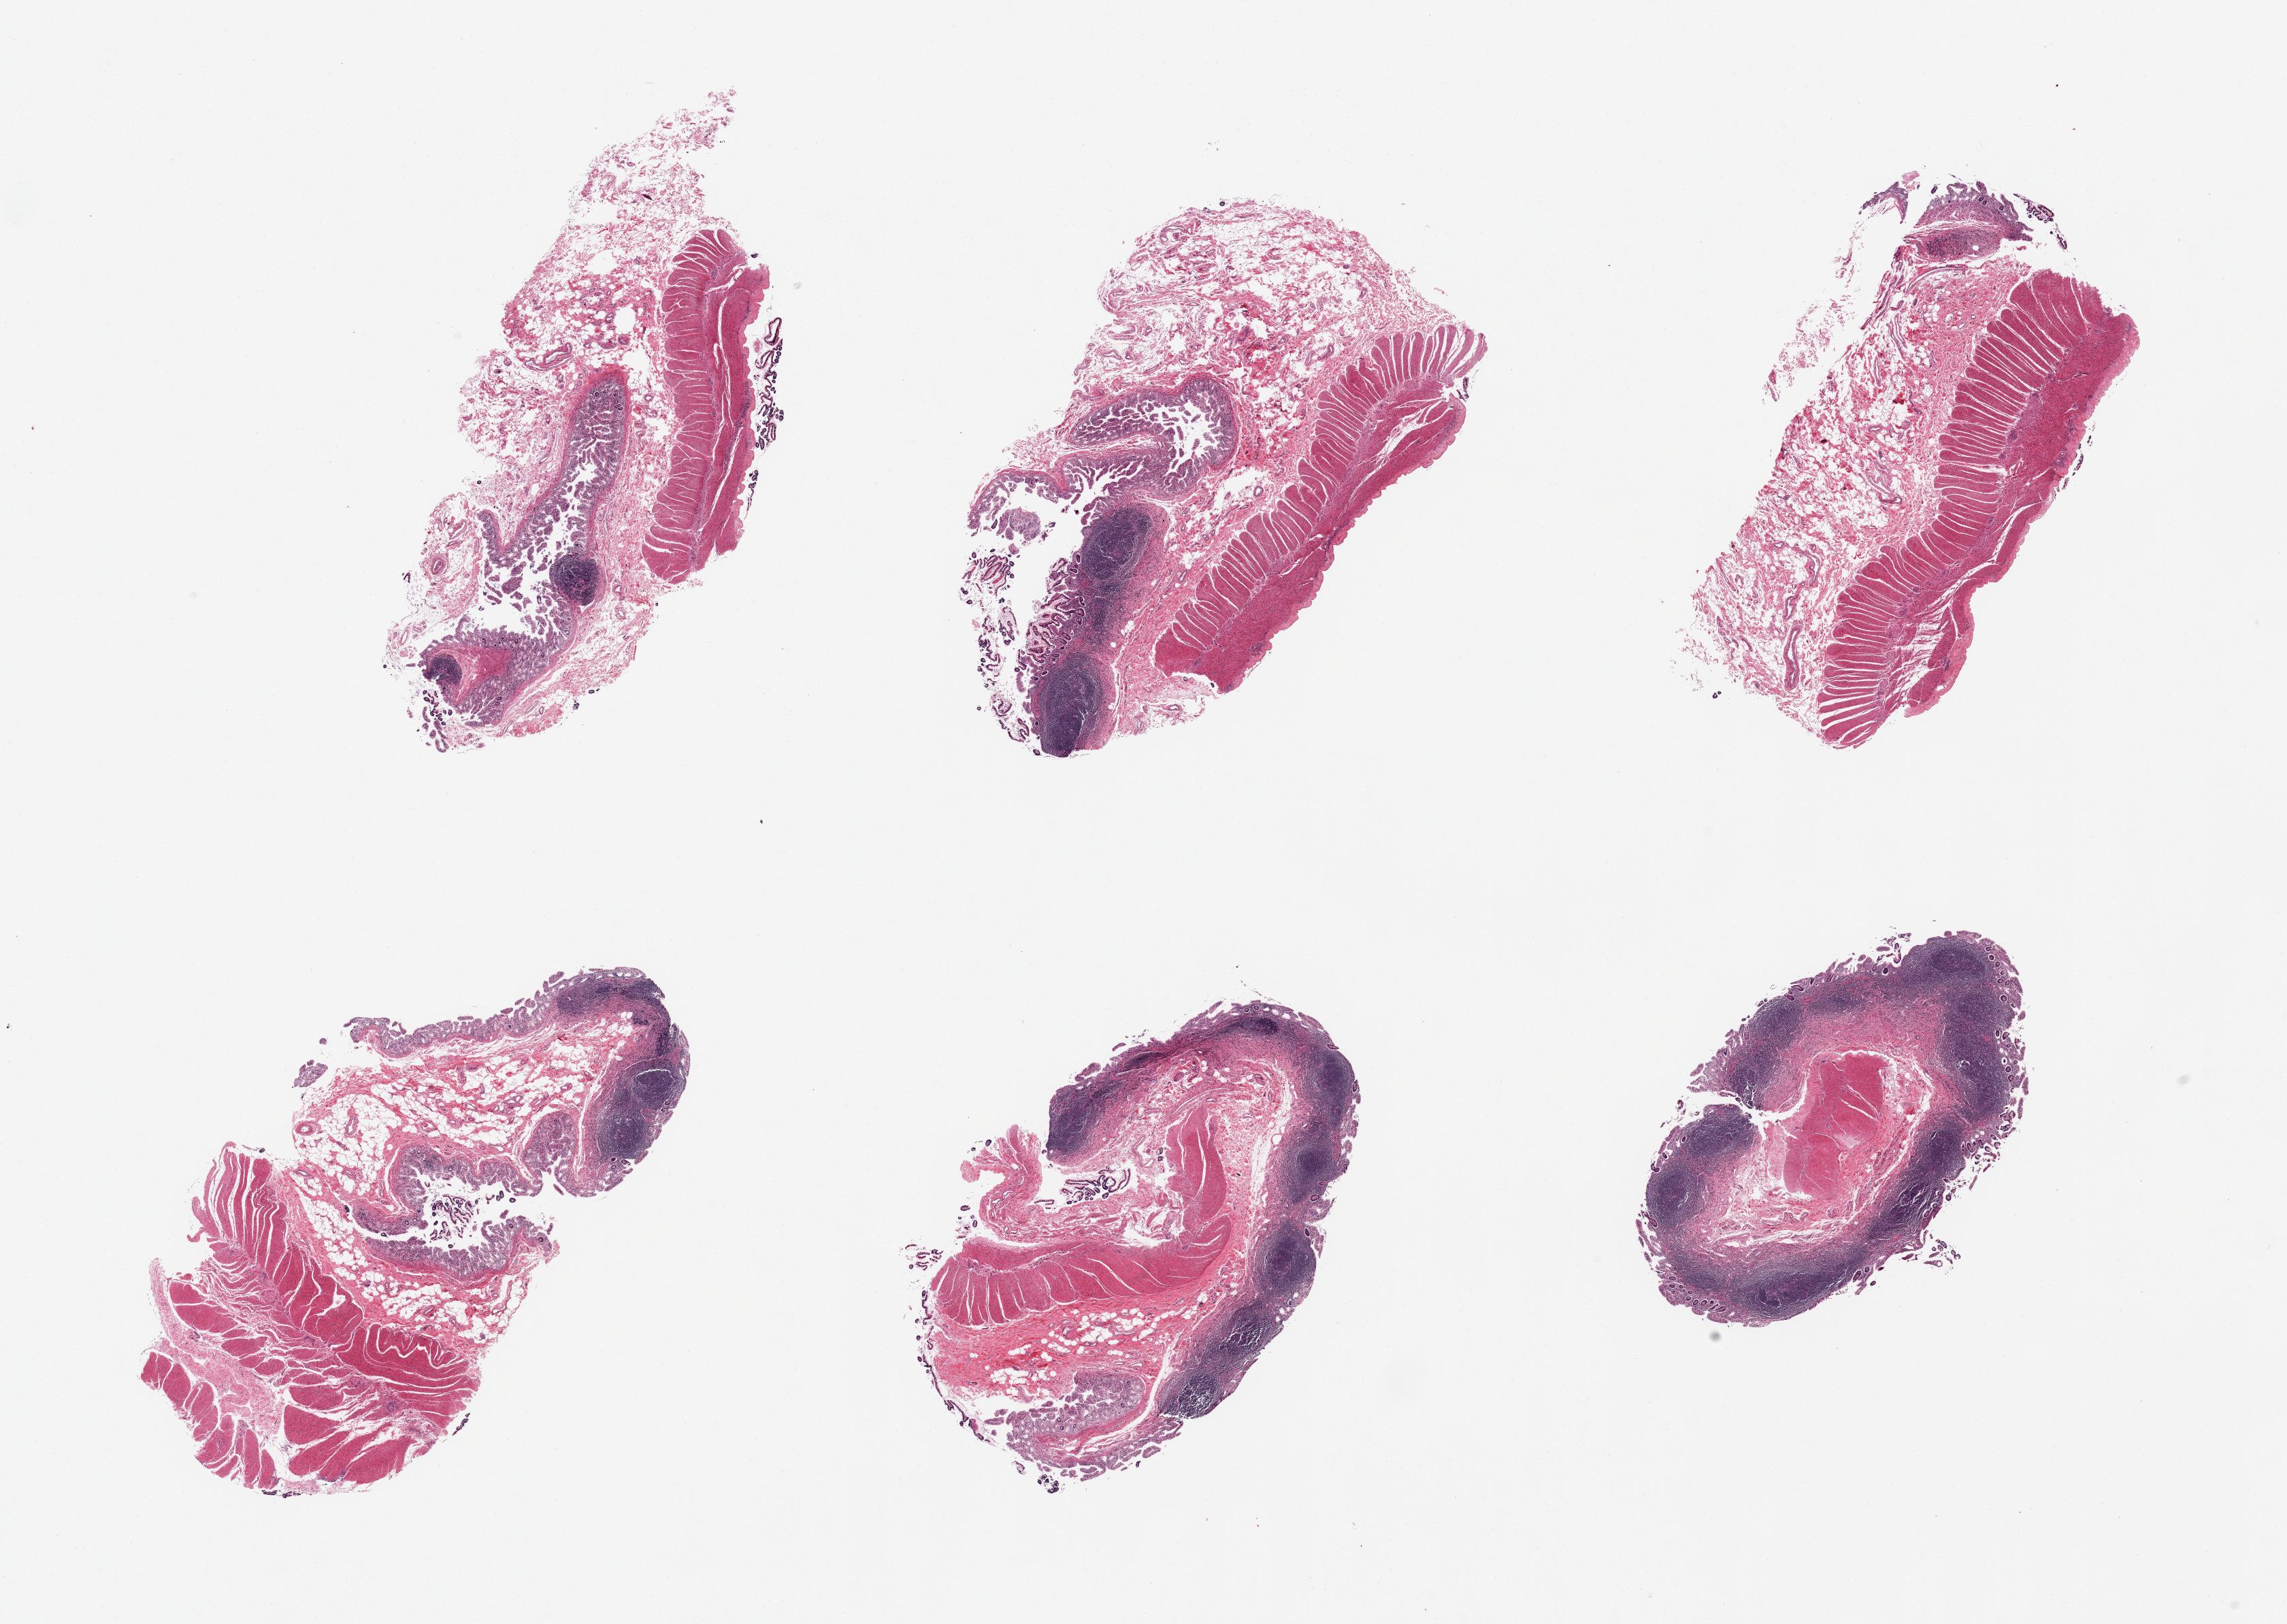
Hematoxylin and eosin (H&E) whole-slide image, whole scanned area (about 26.6 x 18.9 mm) shown as a low-resolution overview; PAXgene-fixed, paraffin-embedded tissue; sampled site (target tissue): ileum; tissue donor sample. Donor: female.
* reviewer comment on this tissue sample: 6 pieces, target lymphoid aggregates are ~20% tissue